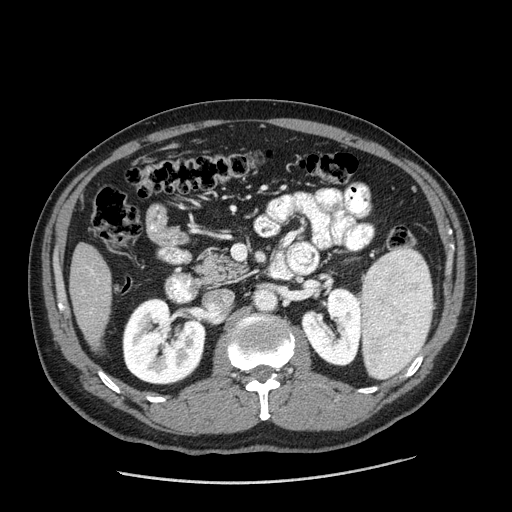
Contrast-enhanced abdominal CT (liver protocol), one axial slice; position 63 of 198 along the scan axis; reconstruction kernel STANDARD; one of 2 acquisitions stored at this slice position; soft-tissue window (W 400 / L 40 HU); 2.5 mm slice thickness; 512 × 512 image matrix. Case-level facts recorded for this patient, not image findings: diagnosis: hepatocellular carcinoma (patient treated with transarterial chemoembolisation; whether this scan precedes or follows treatment is not stated here); TNM stage (as recorded): Stage-II; Child-Pugh class: A; tumour differentiation: moderately differentiated; tumour size: 2.6 cm.
Annotated regions visible in this slice (semi-automatically segmented with operator editing):
- liver parenchyma outside the tumour (the mass and vessels are separate outlines, so this box may not span the whole liver): bounding box (x1, y1, x2, y2) in pixels: (70, 242, 112, 350)